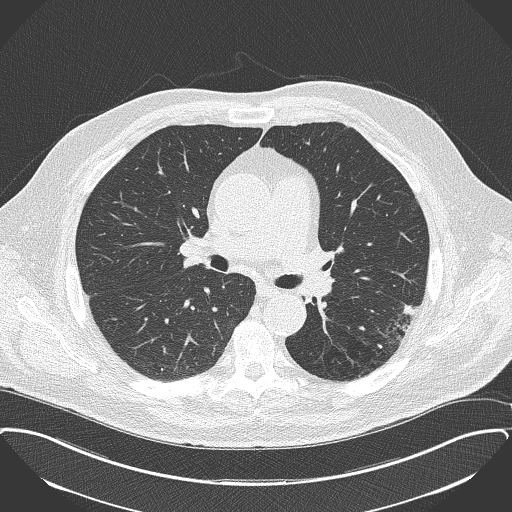
Axial slice from a low-dose chest CT screening exam; second screening round (one year after baseline); lung window (W 1500 / L -600 HU); lung (sharp) reconstruction kernel (B50f); slice 73 of 175 in the series; 512 × 512 image matrix, field of view 400 × 400 mm. Male, age 68 years at enrolment.
Lesion marked by an expert reader, bounding box (x1, y1, x2, y2) in pixels: (371, 293, 428, 347). The screening reader recorded 2 non-calcified nodules or masses ≥4 mm on this exam (left lower lobe, left lower lobe); which of them this box marks is not recorded. Participant outcome: lung cancer diagnosed 126 days after this screen — adenocarcinoma, NOS, left lower lobe, poorly differentiated (G3), stage IB (AJCC 6th edition), 17 mm at pathology.